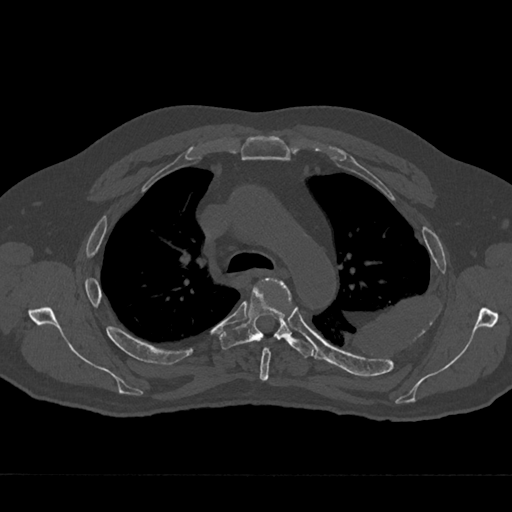
CT including the spine, one axial slice. 120 kVp. Bone window (W 1800 / L 400 HU). 0.5 mm slice thickness. 512 × 512 image matrix, field of view 377 × 377 mm. Patient: male, 75 years. From the clinical record (not read from this slice): primary cancer: renal; vertebrae with lytic lesions (as recorded): T4.
Outlined on this slice (semi-automatically segmented with operator editing):
- T4 vertebra: bounding box <260,280,291,381> (left, top, right, bottom; pixels)
- T5 vertebra: <219,278,314,358>